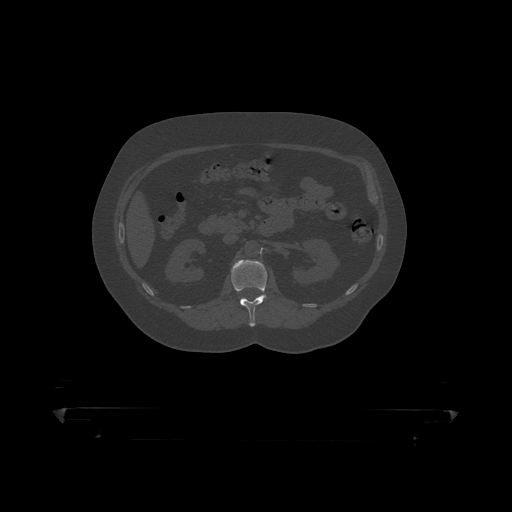
CT including the spine, one axial slice. Position 140 of 390 along the scan axis. 120 kVp. Bone window (W 1800 / L 400 HU). 512 × 512 image matrix, field of view 650 × 650 mm. Patient: male, 60 years. Case-level facts recorded for this patient, not image findings: primary cancer: prostate.
Outlined on this slice (semi-automatic segmentation, software-assisted and operator-edited):
- L1 vertebra: bounding box [x1, y1, x2, y2] px = [232, 260, 270, 319]